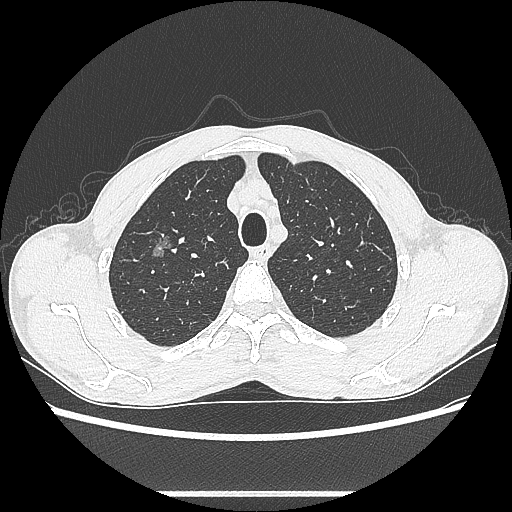
Chest CT, one axial slice; position 480 of 601 along the scan axis; reconstruction kernel LUNG; 100 kVp; lung window (W 1500 / L -600 HU); 0.62 mm slice thickness; 512 × 512 image matrix, field of view 357 × 357 mm. Male patient, age 54 years. From the clinical record (not read from this slice): clinical TNM (as recorded): T1a N0 M0.
Annotated regions visible in this slice (bounding box drawn by a radiologist):
- lung tumour (recorded histology: adenocarcinoma): box from (x=145, y=230) to (x=175, y=265) px